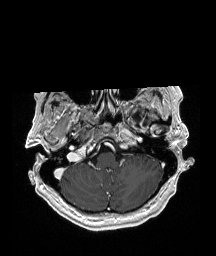
Brain MRI from a brain-tumour surgery series, one axial slice; position 152 of 192 along the scan axis; T1-weighted post-contrast; 1 mm slice thickness; 216 × 256 image matrix, field of view 211 × 250 mm. Case-level facts recorded for this patient, not image findings: histopathology: Glioblastoma; WHO grade: 4; IDH mutation: no; tumour location: Left Temporal.
Structures marked on this image (outlined manually by an expert reader):
- previous resection cavity: box from (x=130, y=112) to (x=146, y=127) px